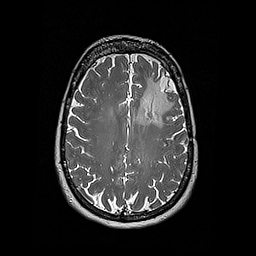
Brain MRI from a brain-tumour surgery series, one axial slice; position 124 of 192 along the scan axis; 256 × 256 image matrix, field of view 250 × 250 mm. Case-level facts recorded for this patient, not image findings: histopathology: Oligodendroglioma; WHO grade: 2; IDH mutation: yes; tumour location: Left Frontal.
Outlined on this slice (outlined manually by an expert reader):
- tumour: bounding box <136,73,175,128> (left, top, right, bottom; pixels)